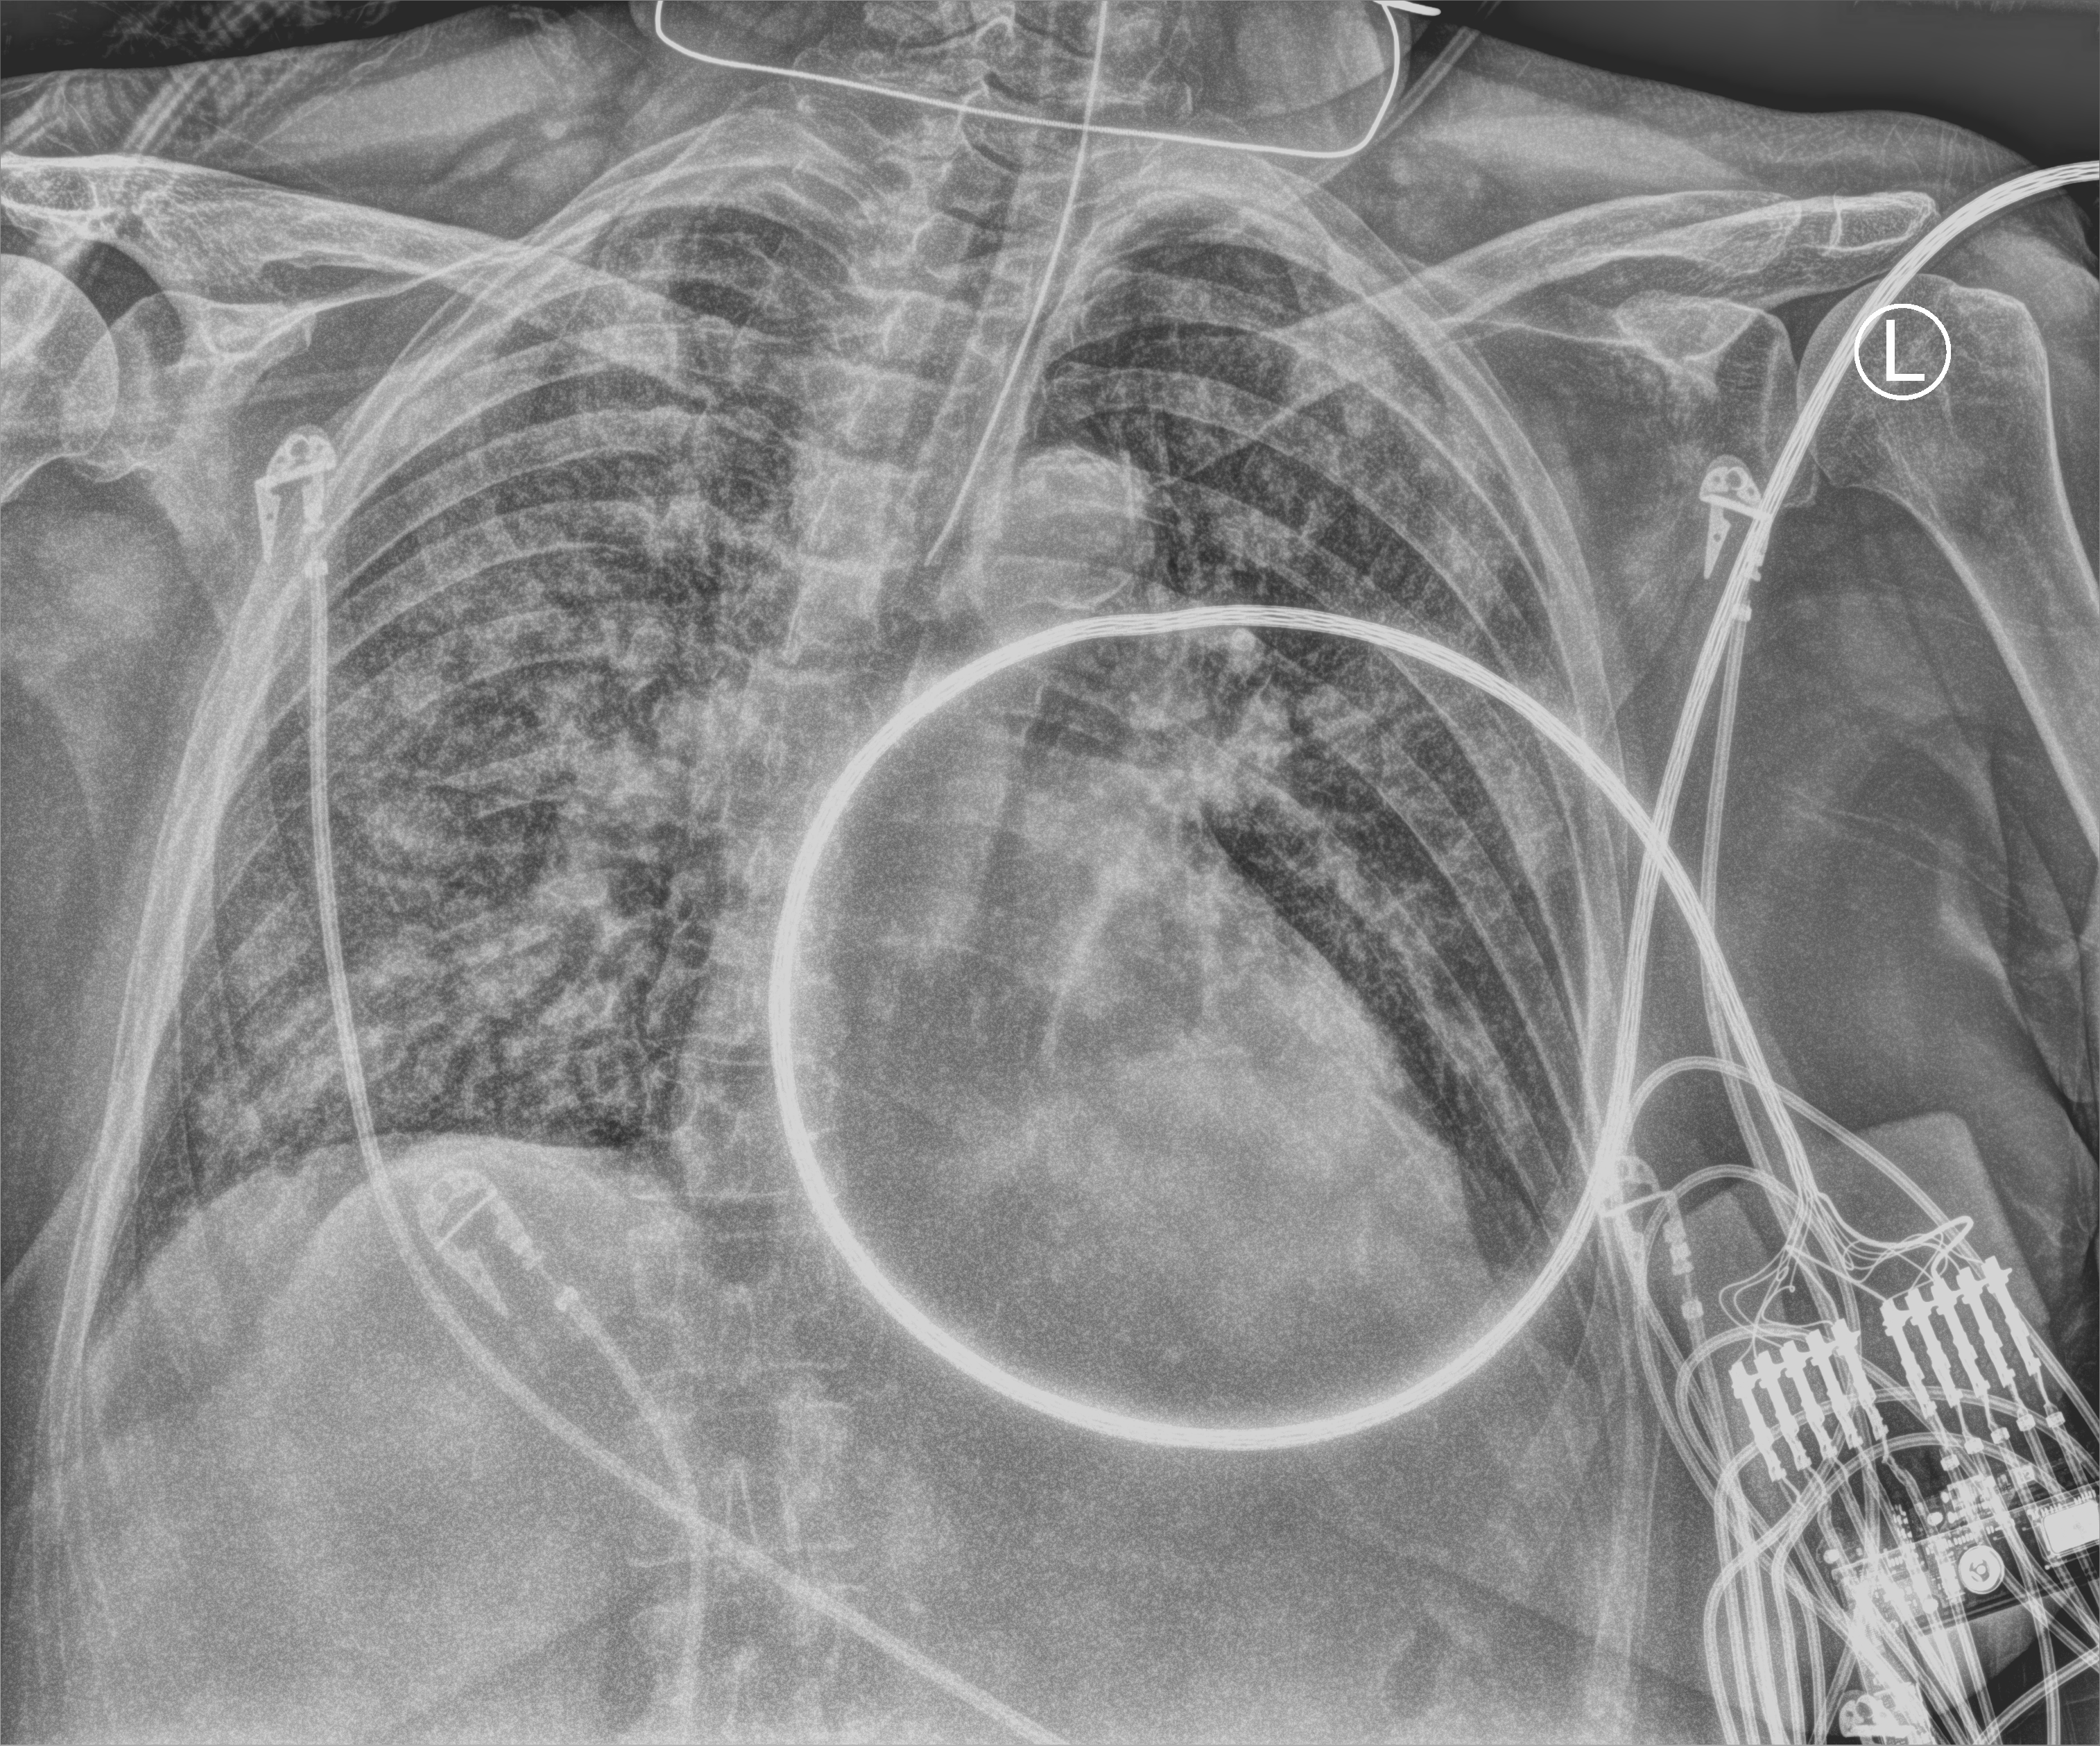
Chest X-ray (portable). Female patient hospitalised with COVID-19, age 75–90 years.
From the hospital-stay record, not from the radiograph (when in the stay this image was taken is not recorded):
- admitted to intensive care during this hospital stay: yes
- mechanically ventilated during this hospital stay: yes